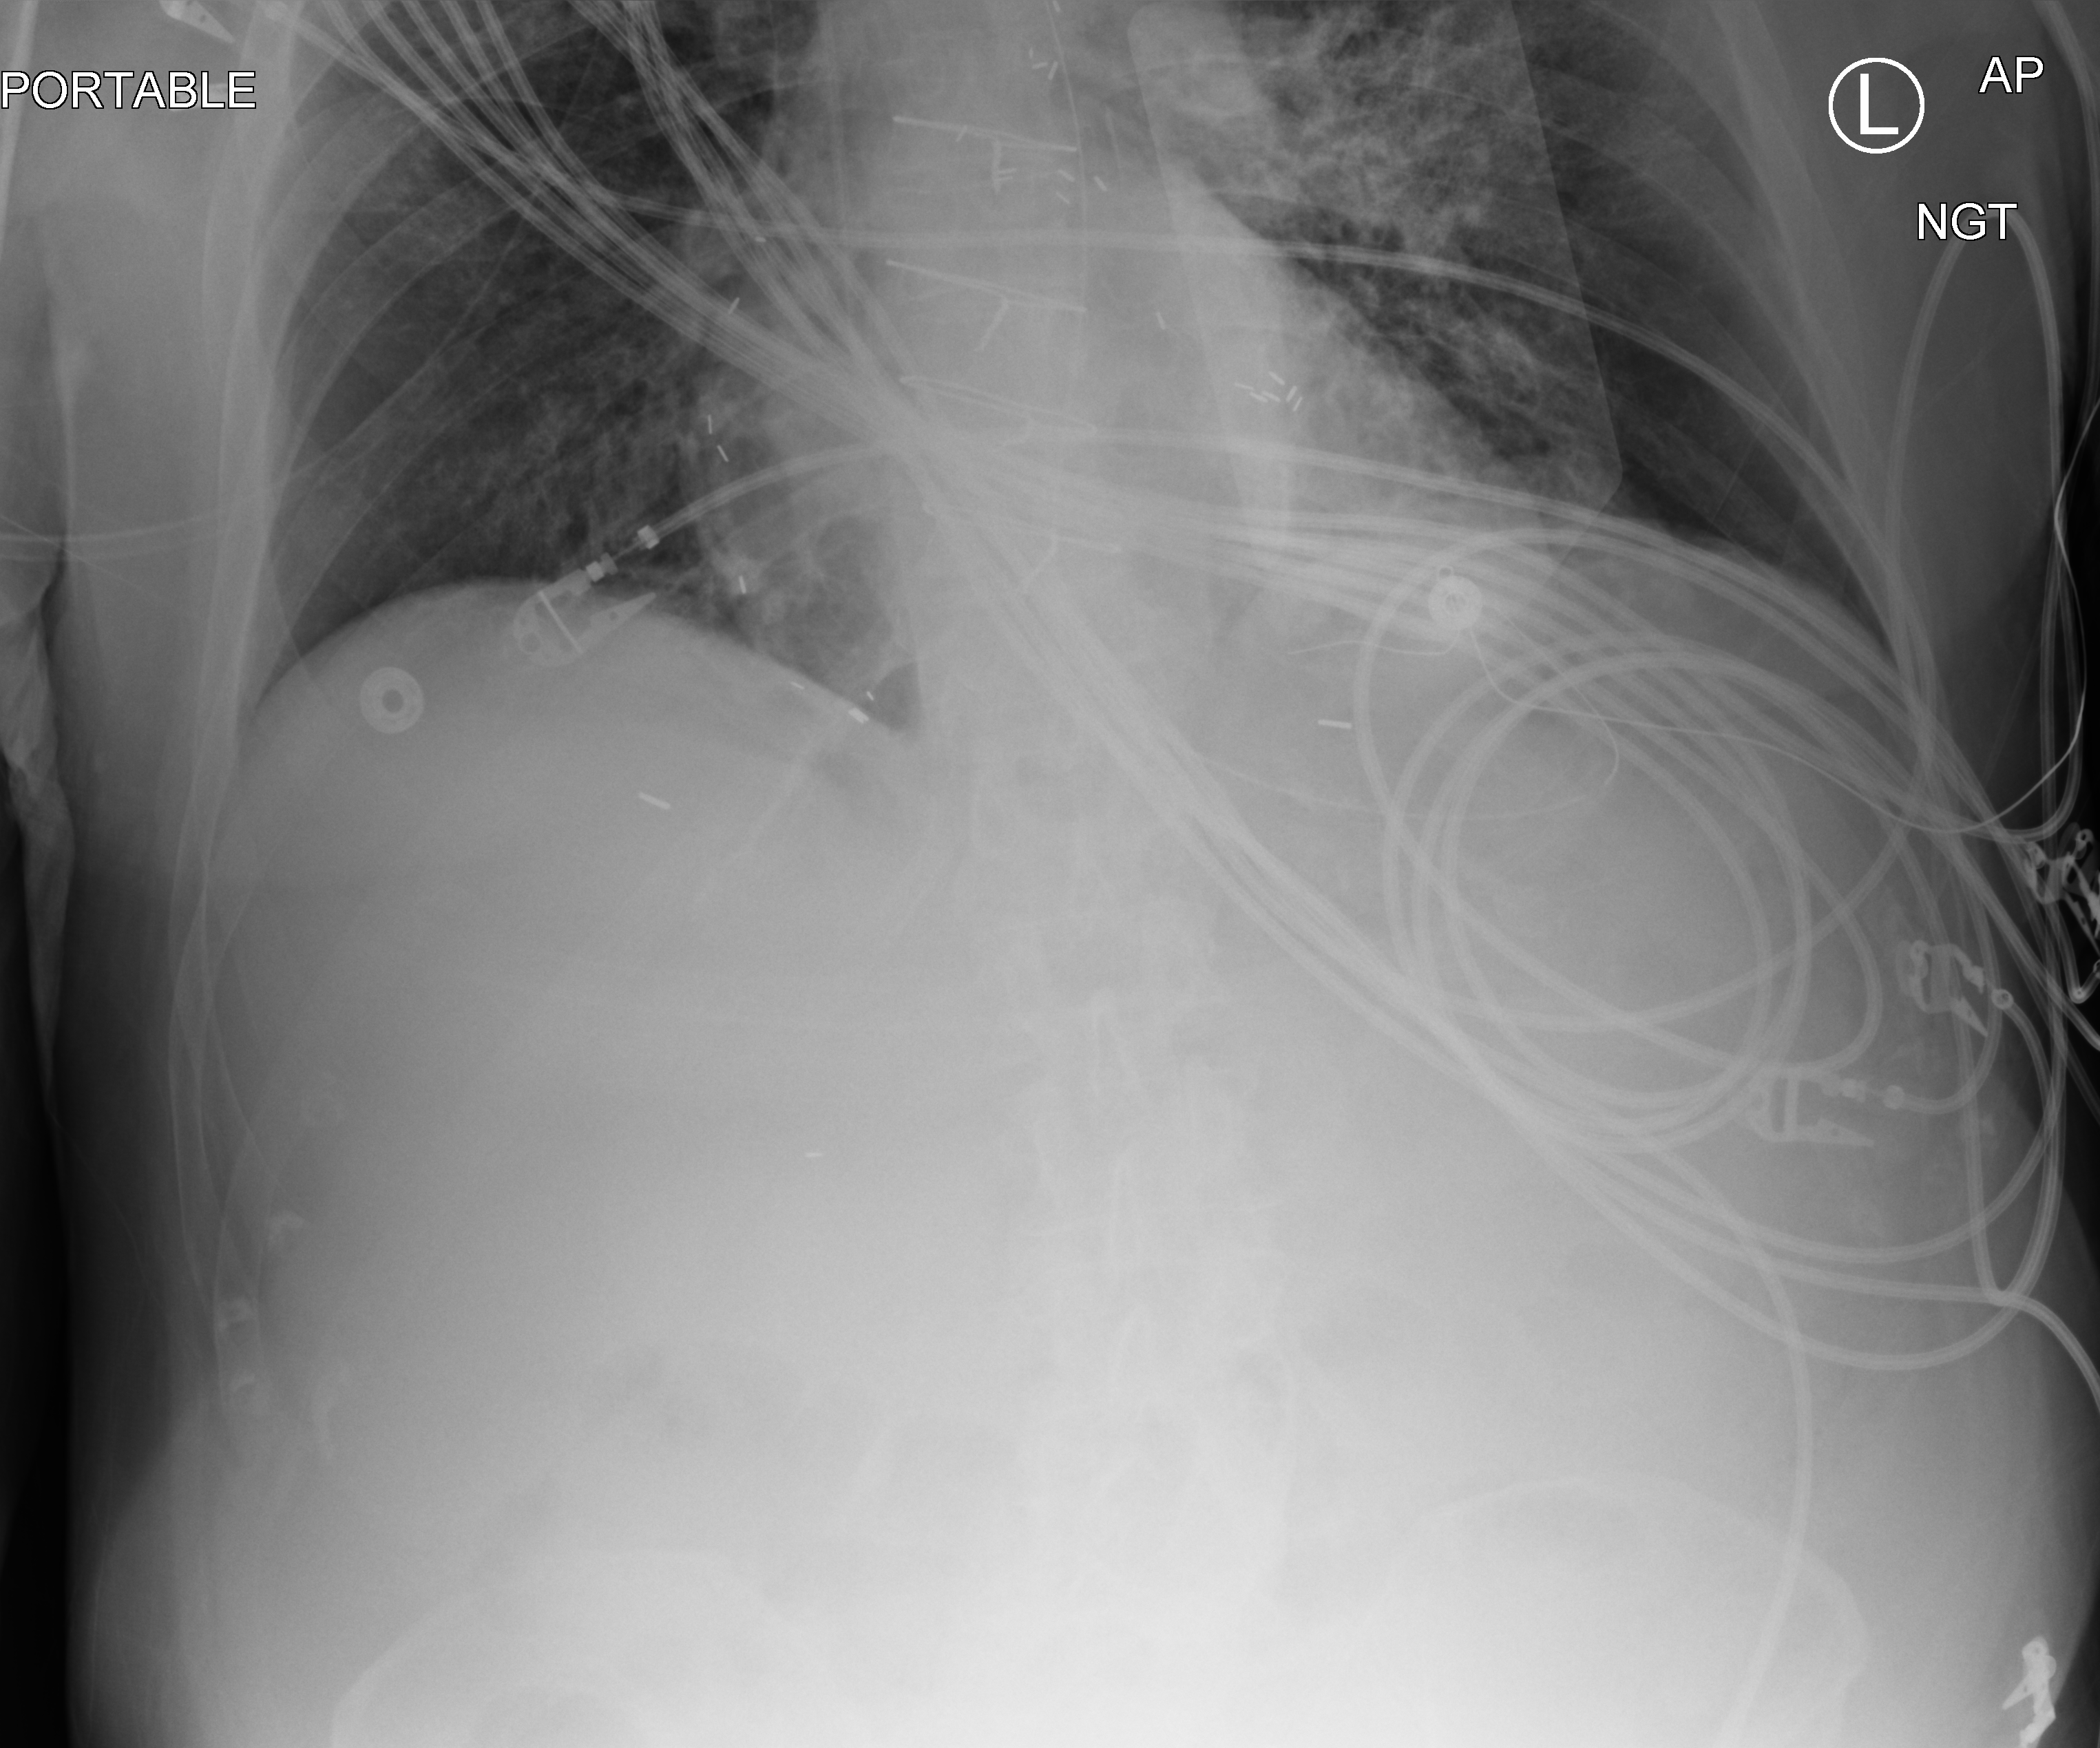
Bedside chest radiograph (computed radiography), anteroposterior (AP) projection. Male patient hospitalised with COVID-19, age 75–90 years.
Hospital-stay facts (about this admission, not read from this image; timing relative to this image not recorded):
- chronic kidney disease (admission record): no
- mechanically ventilated during this hospital stay: yes